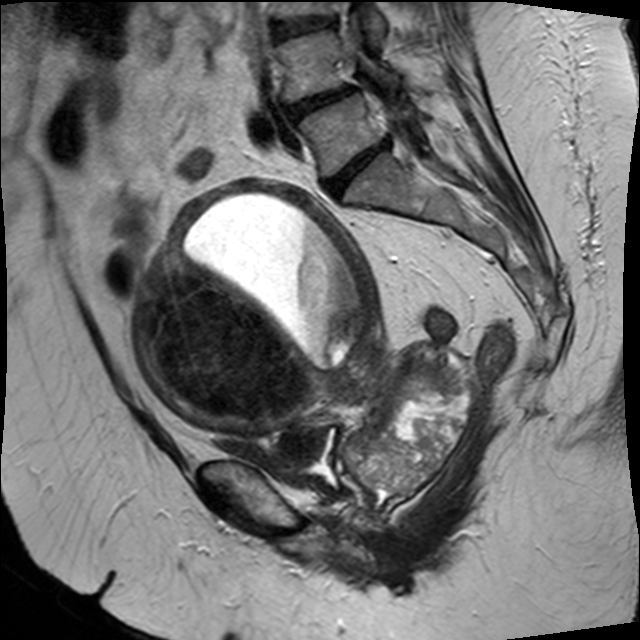
Pelvic MRI for cervical cancer, one sagittal slice; position 20 of 34 along the scan axis; T2-weighted; 1.5 T; TE 89 ms, TR 3320 ms; 4 mm slice thickness; 640 × 640 image matrix, field of view 260 × 260 mm. Patient: female, 50 years.
Outlined on this slice (outlined manually by an expert reader):
- uterus and cervix: bounding box <128,179,482,493> (left, top, right, bottom; pixels)